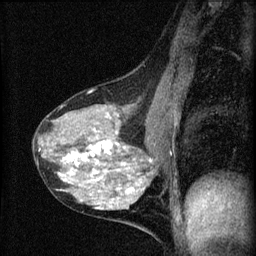
Breast MRI (dynamic contrast-enhanced), one sagittal slice. Dynamic contrast-enhanced series, image 2 of 4 at this slice position (ordered by acquisition). 1.5 T. TE 4.2 ms, TR 8.2 ms. 256 × 256 image matrix, field of view 180 × 180 mm. Female patient, age 41 years.
Annotated regions visible in this slice (semi-automatic segmentation, software-assisted and operator-edited):
- analysis volume of interest (the breast-tissue region the enhancement analysis was run in; not a lesion): box from (x=33, y=91) to (x=166, y=210) px
- tumour enhancement mask (voxels above the 70 % enhancement threshold inside the analysis volume of interest): (x=39, y=123)–(x=151, y=209)